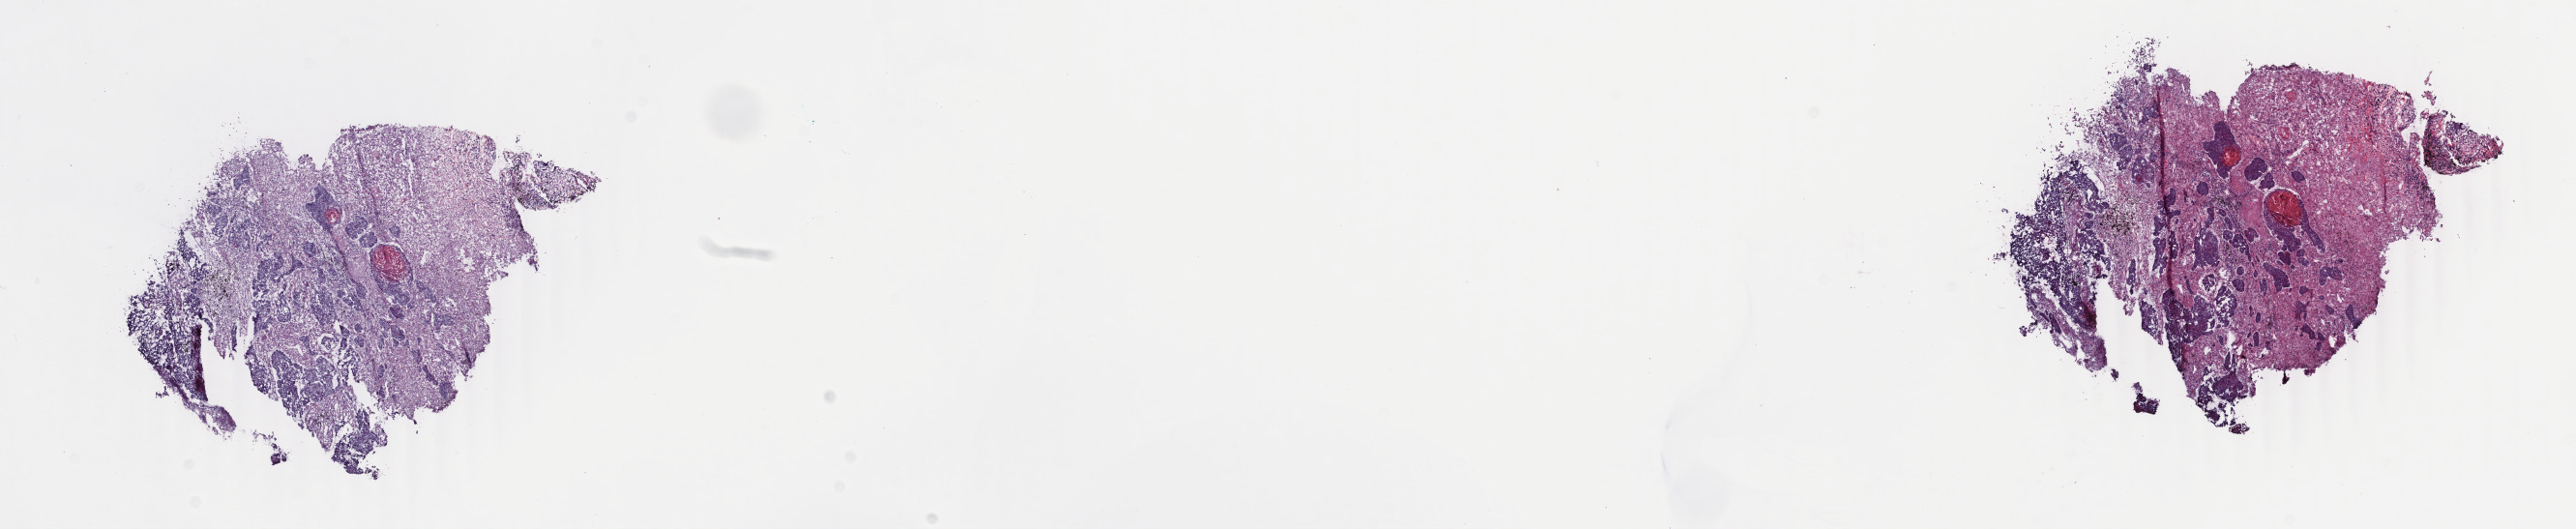
H&E whole-slide image — whole scanned area (about 21.2 x 4.4 mm, slide scanned at 40x) shown as a low-resolution overview. Frozen section from the top of the tissue portion. Lung, primary tumour sample. Patient: male, age at initial diagnosis 69 years. Composition of this section per pathologist review: tumour cells 65%, tumour nuclei 65%, normal cells 0%, stromal cells 30%, necrosis 5%. Inflammatory infiltration, as recorded: lymphocyte infiltration 4%, monocyte infiltration 2%, neutrophil infiltration 2%.
AJCC pathologic stage: IB (7th edition). Pathologic diagnosis: Squamous cell carcinoma, NOS (upper lobe, lung).